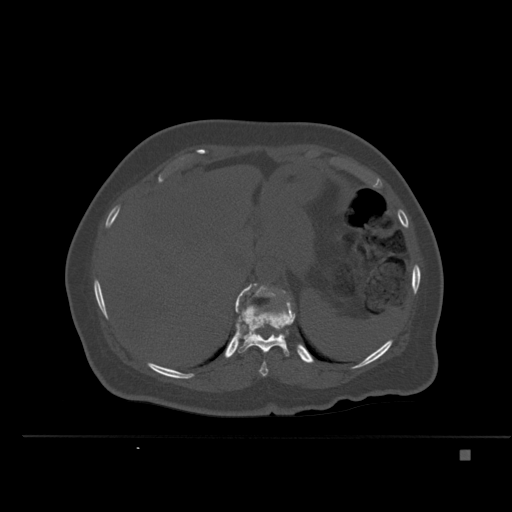
CT including the spine, one axial slice; slice 268 of 477 in the series (ordered by position); bone window (W 1800 / L 400 HU); 512 × 512 image matrix, field of view 422 × 422 mm. Female patient, age 74 years. Case-level facts recorded for this patient, not image findings: primary cancer: colon.
Outlined on this slice (semi-automatically segmented with operator editing):
- T10 vertebra: bounding box (x1, y1, x2, y2) in pixels: (259, 361, 268, 377)
- T11 vertebra: (236, 290, 296, 357)
- T12 vertebra: (235, 283, 291, 310)